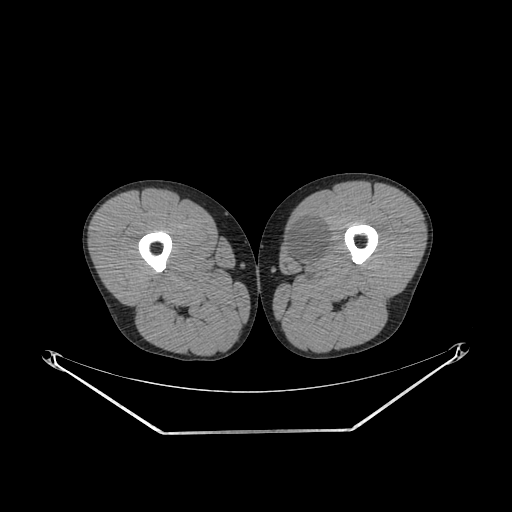
CT of an extremity soft-tissue mass (from a PET/CT study), one axial slice; position 253 of 311 along the scan axis; 140 kVp; soft-tissue window (W 400 / L 40 HU); 3.75 mm slice thickness; 512 × 512 image matrix, field of view 500 × 500 mm. Male patient. Case-level facts recorded for this patient, not image findings: histological type: mixoid liposarcoma; grade: low; site of the primary tumour: left thigh.
Outlined on this slice (expert contour drawn on MRI and transferred to this co-registered scan by the dataset authors):
- gross tumour volume (mass): bounding box <285,219,328,264> (left, top, right, bottom; pixels)